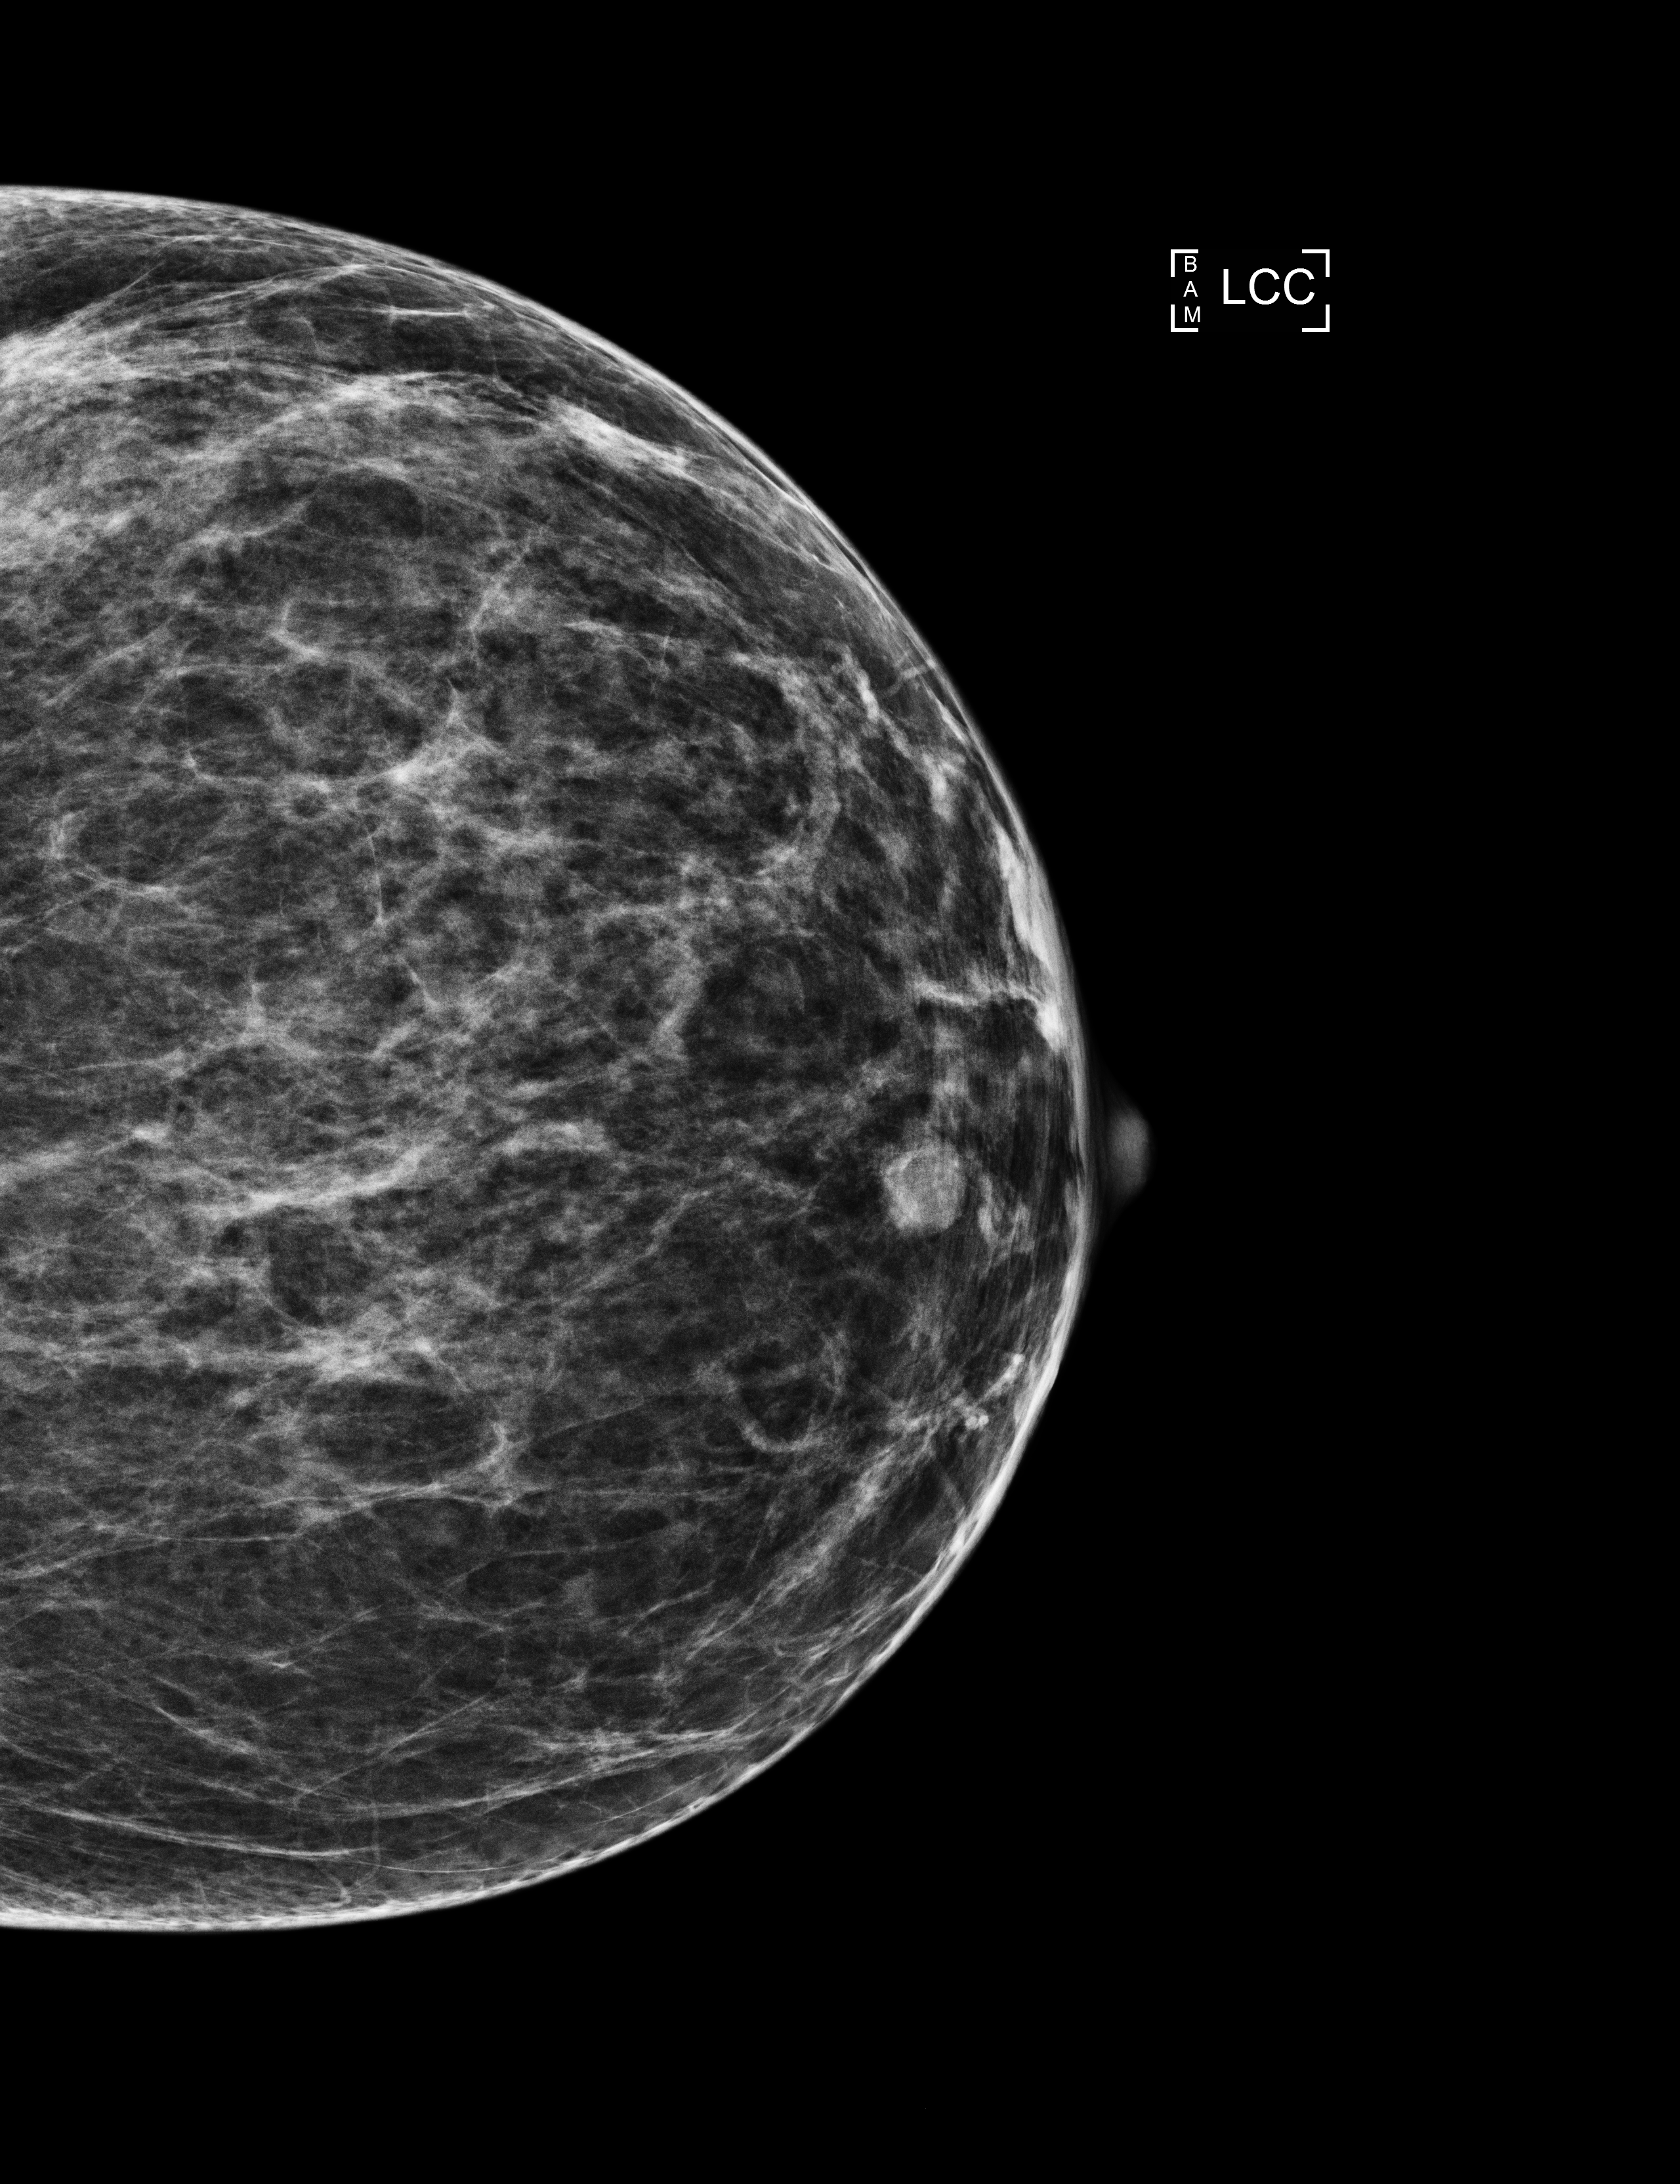
Screening examination. Patient aged 45 years (female).
Image type: full-field digital mammogram. Breast: left. Projection: cranio-caudal projection.